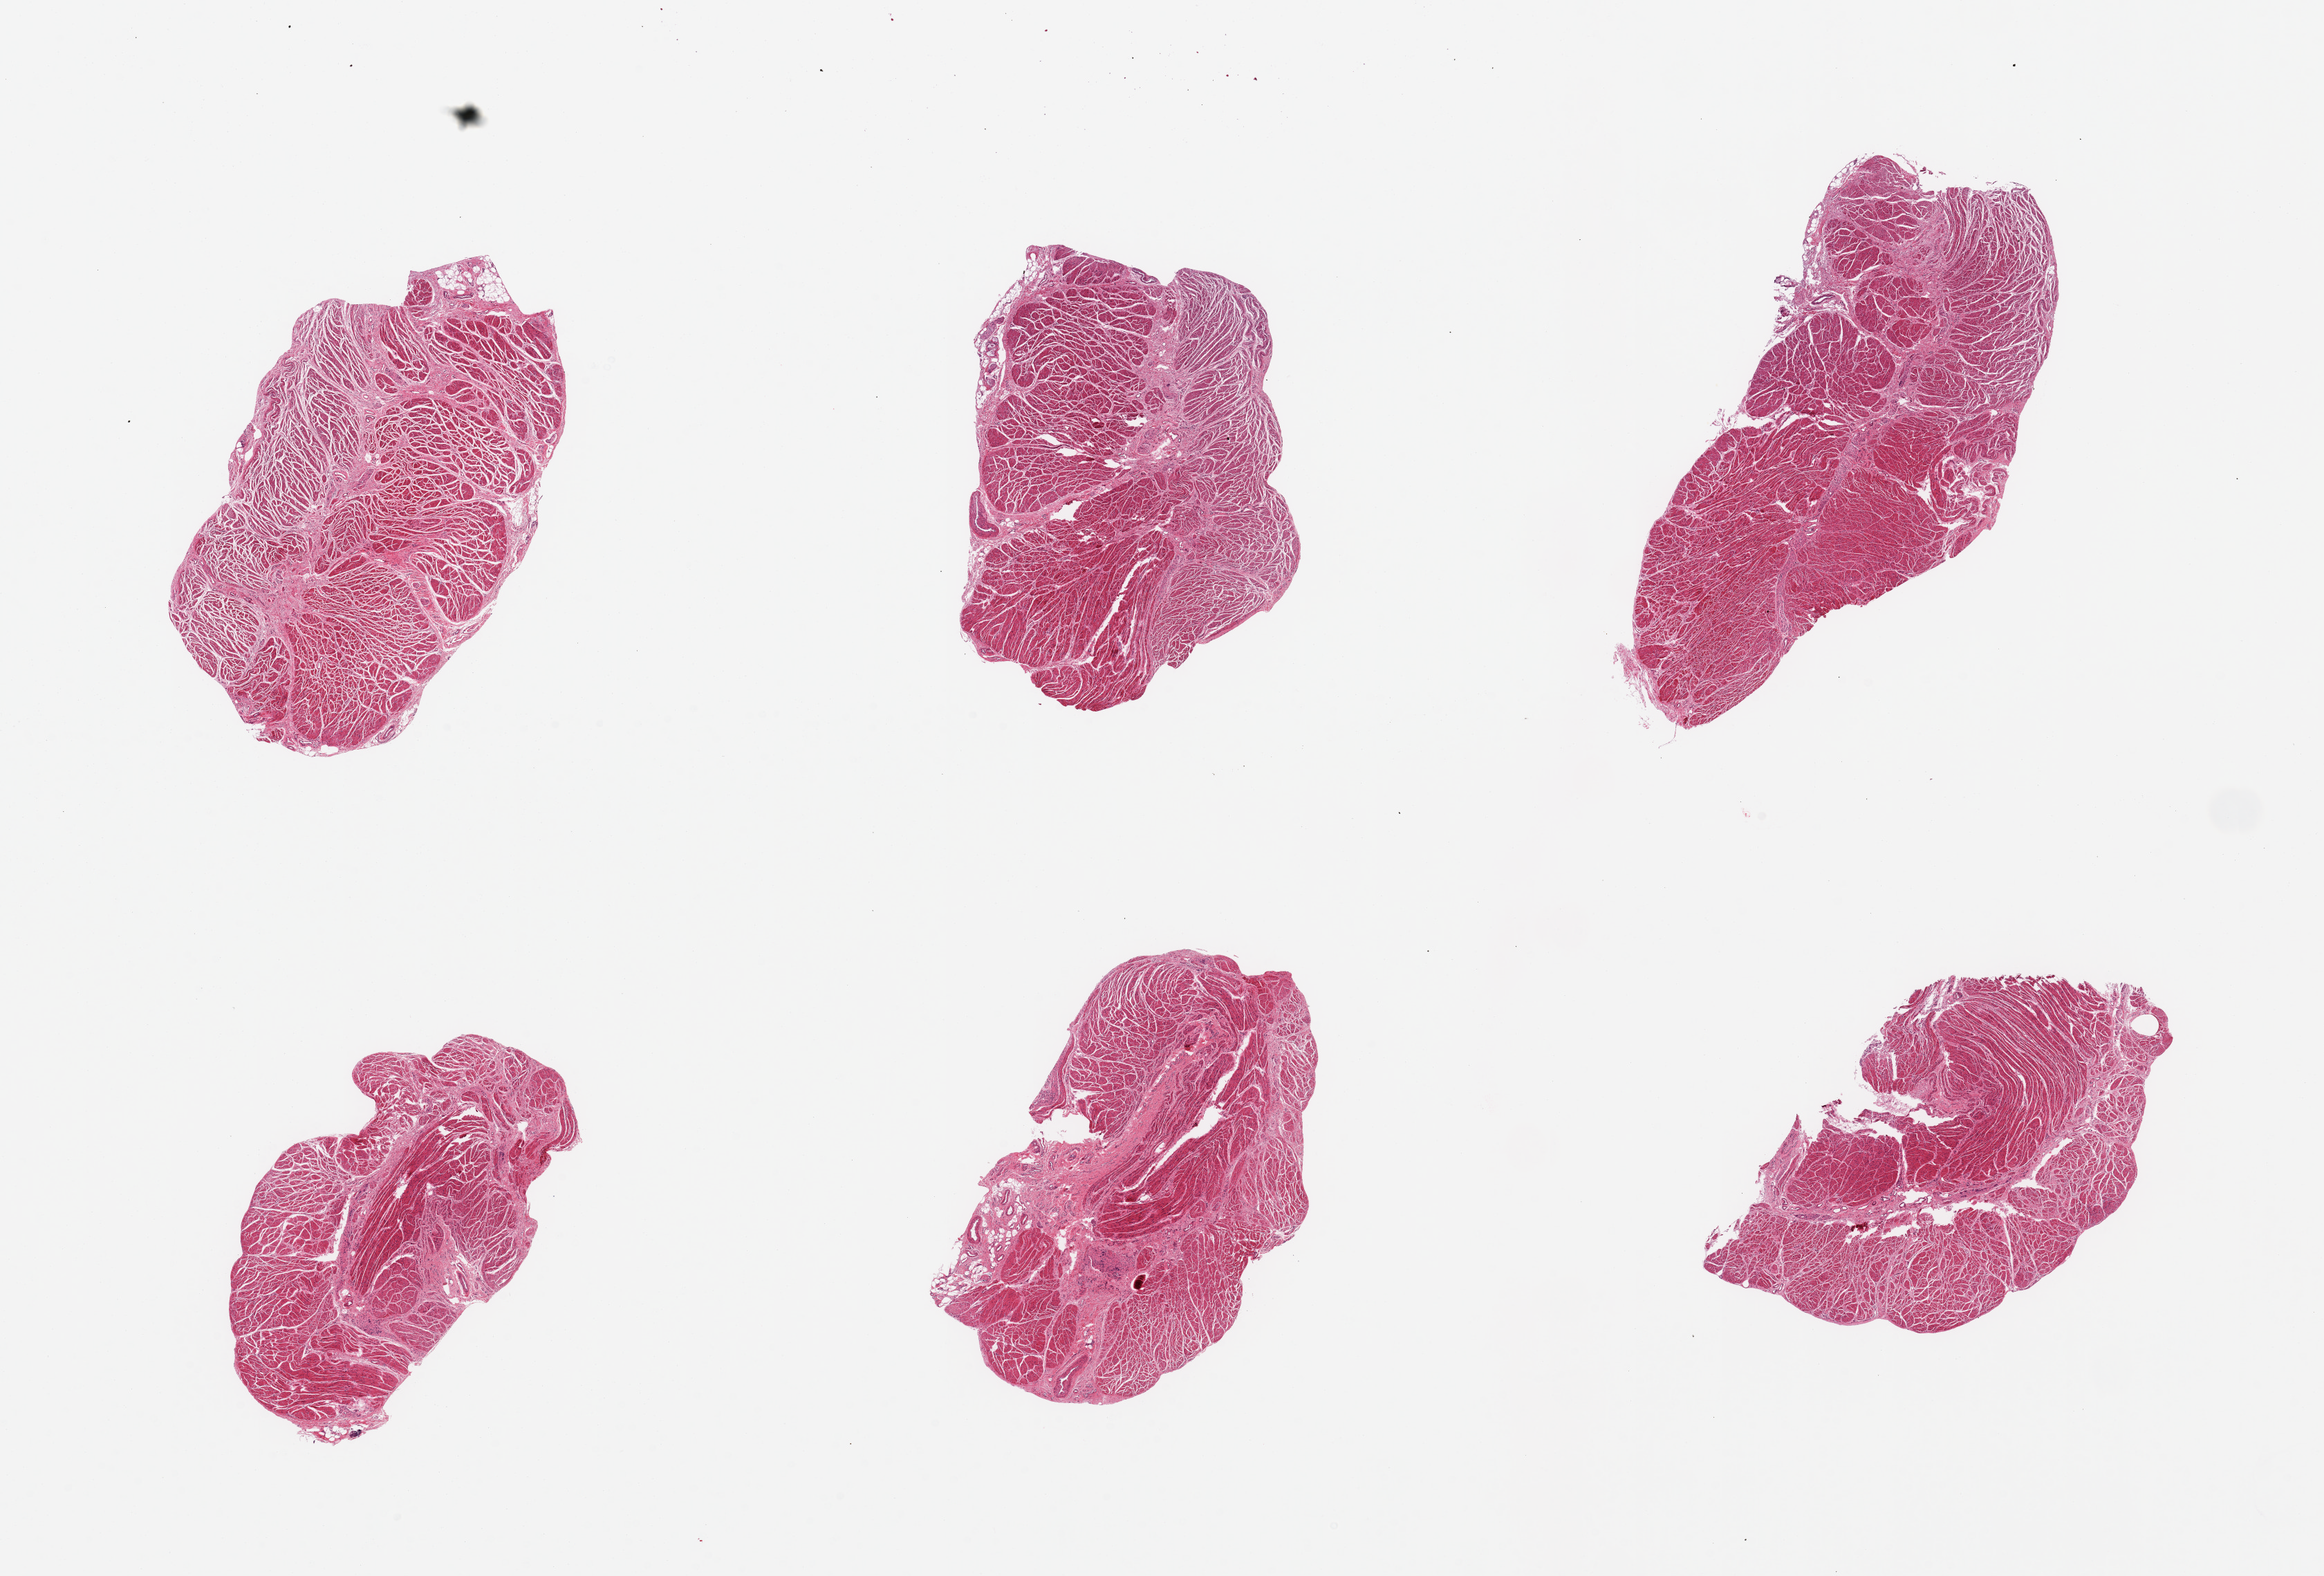
Digitized haematoxylin and eosin-stained section, brightfield, shown as a low-resolution overview of the whole scanned area (about 26.6 x 18.0 mm, acquisition: 20x scan); PAXgene-fixed, paraffin-embedded tissue; target tissue: esophageal muscle; tissue donor sample. Donor sex: female.
Review note (as recorded): 6 pieces; well dissected muscularis propria.